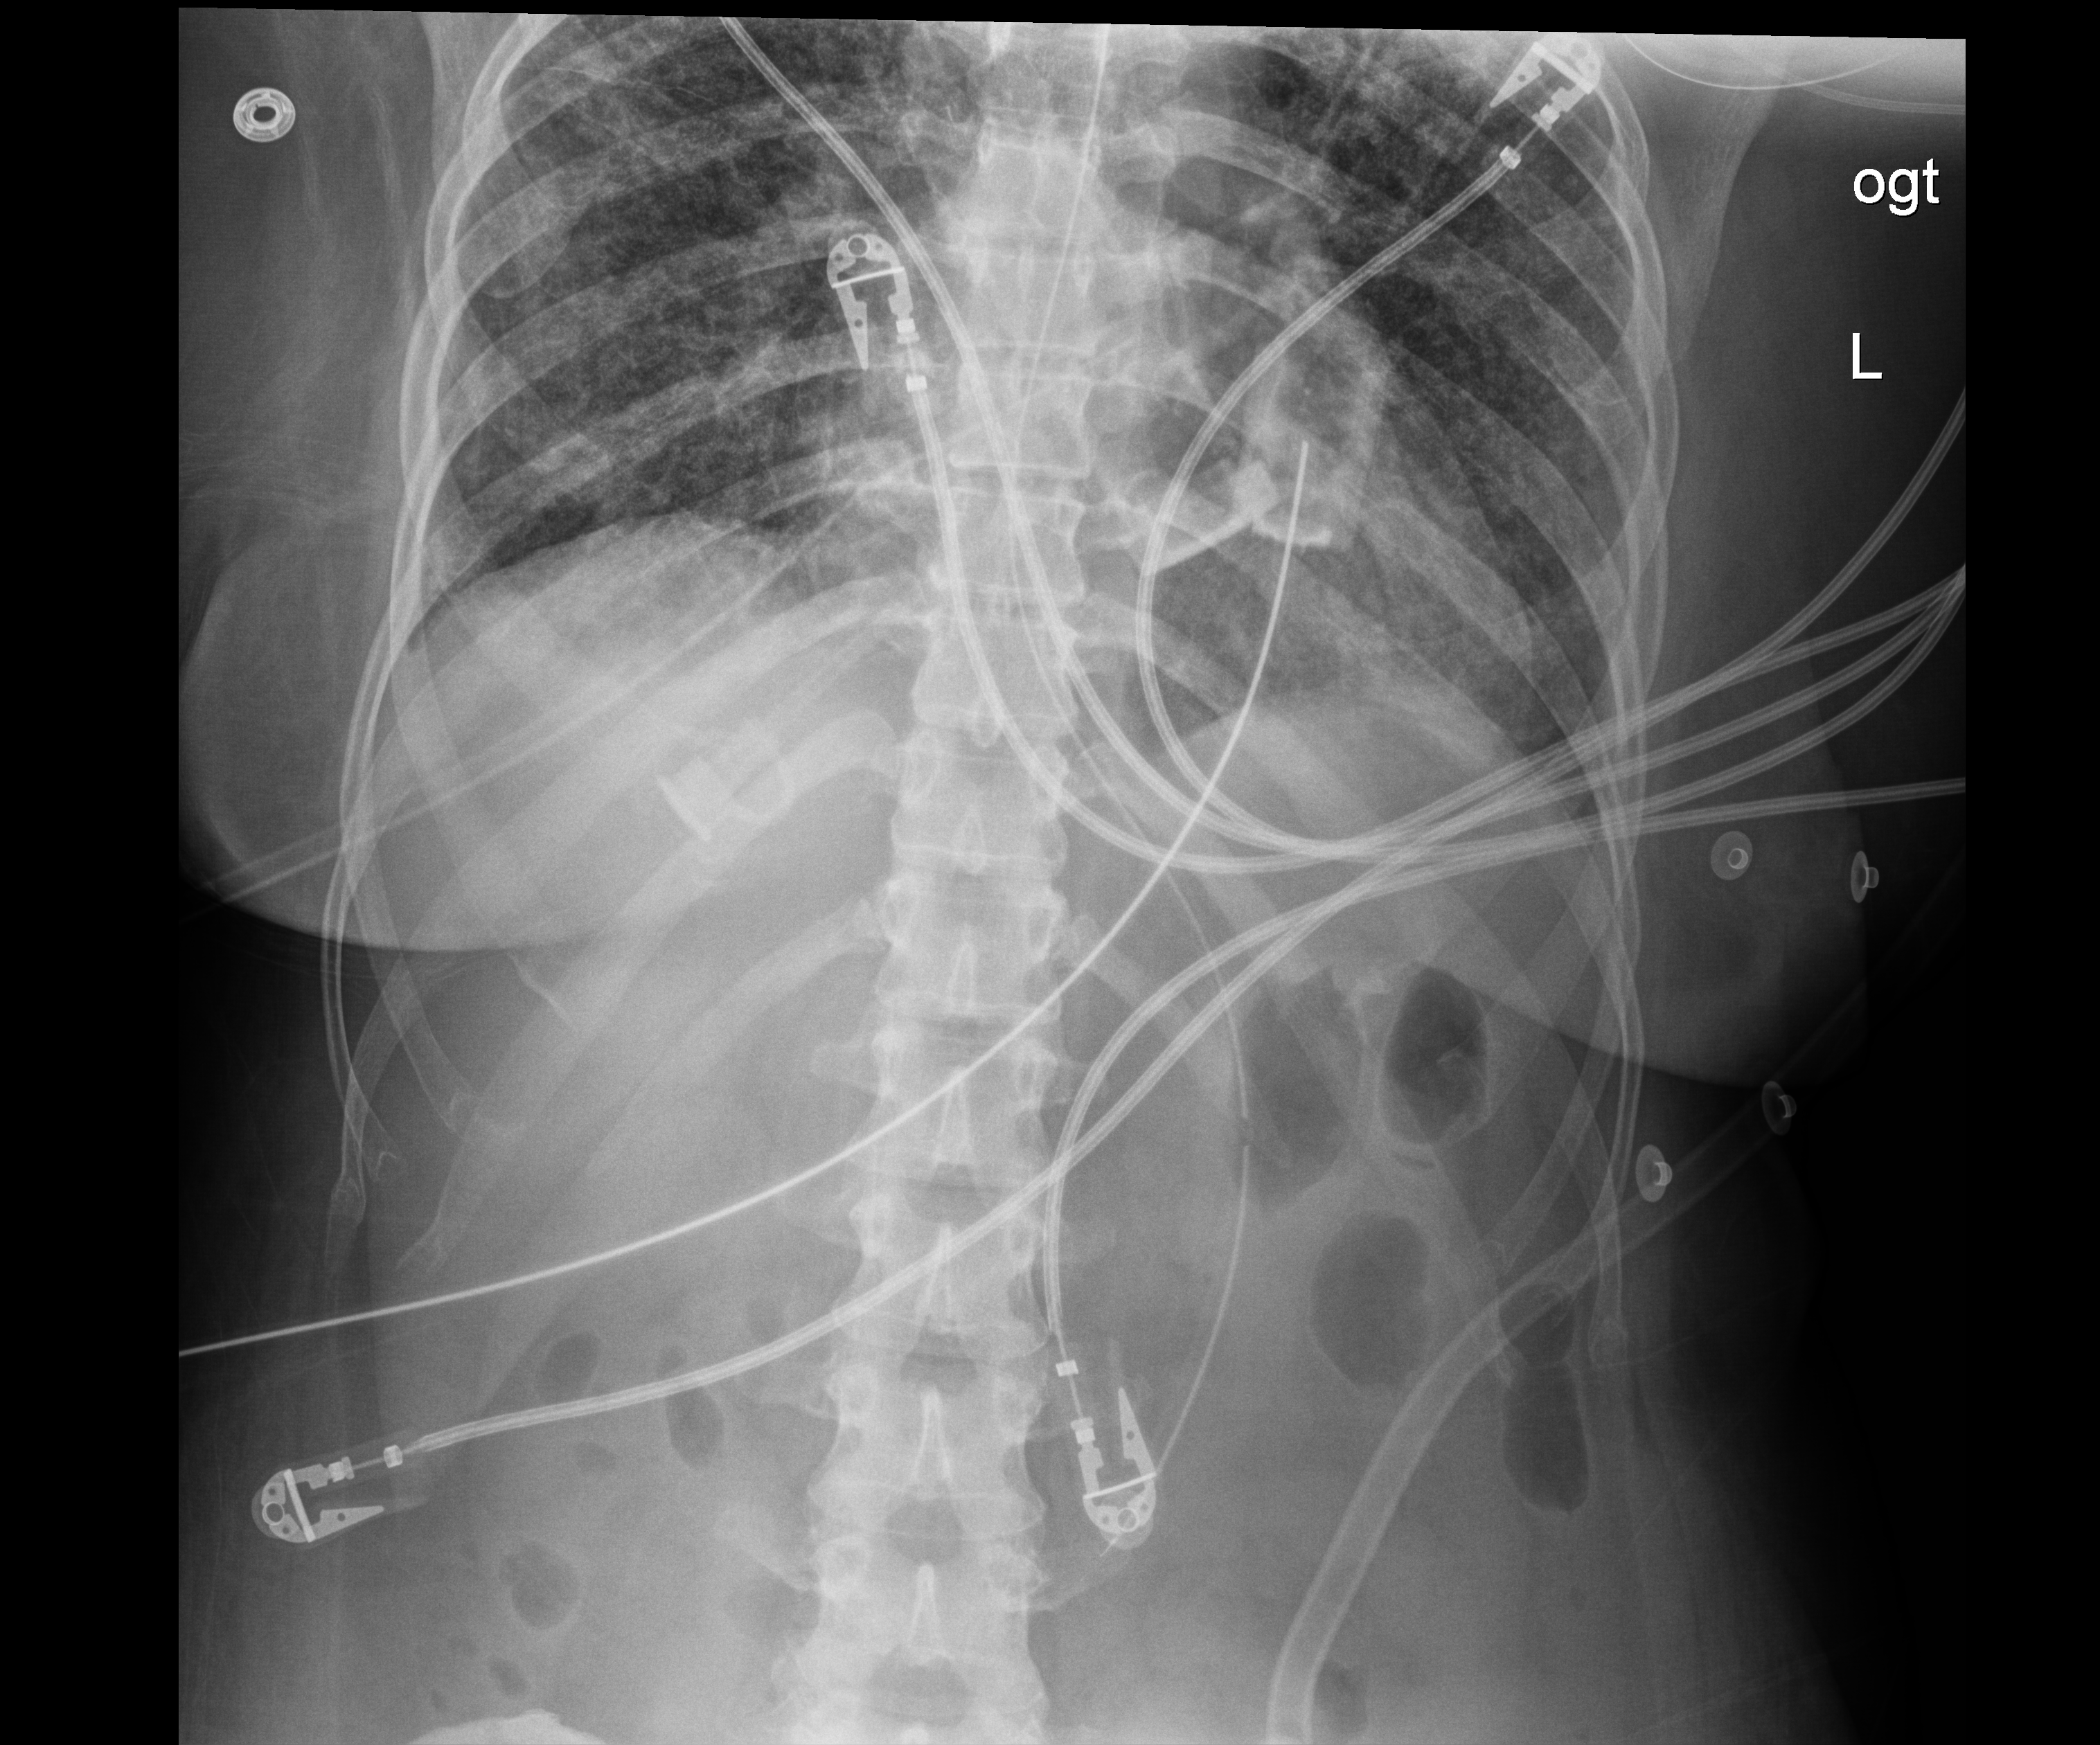
Bedside chest radiograph (digital radiography); anteroposterior (AP) projection. Patient hospitalised with COVID-19; male, aged 18–59 years.
Admission-level facts for this patient (not findings on this image; timing relative to this image not recorded):
- length of hospital stay: 38 days
- admitted to intensive care during this hospital stay: yes
- hypertension (admission record): yes